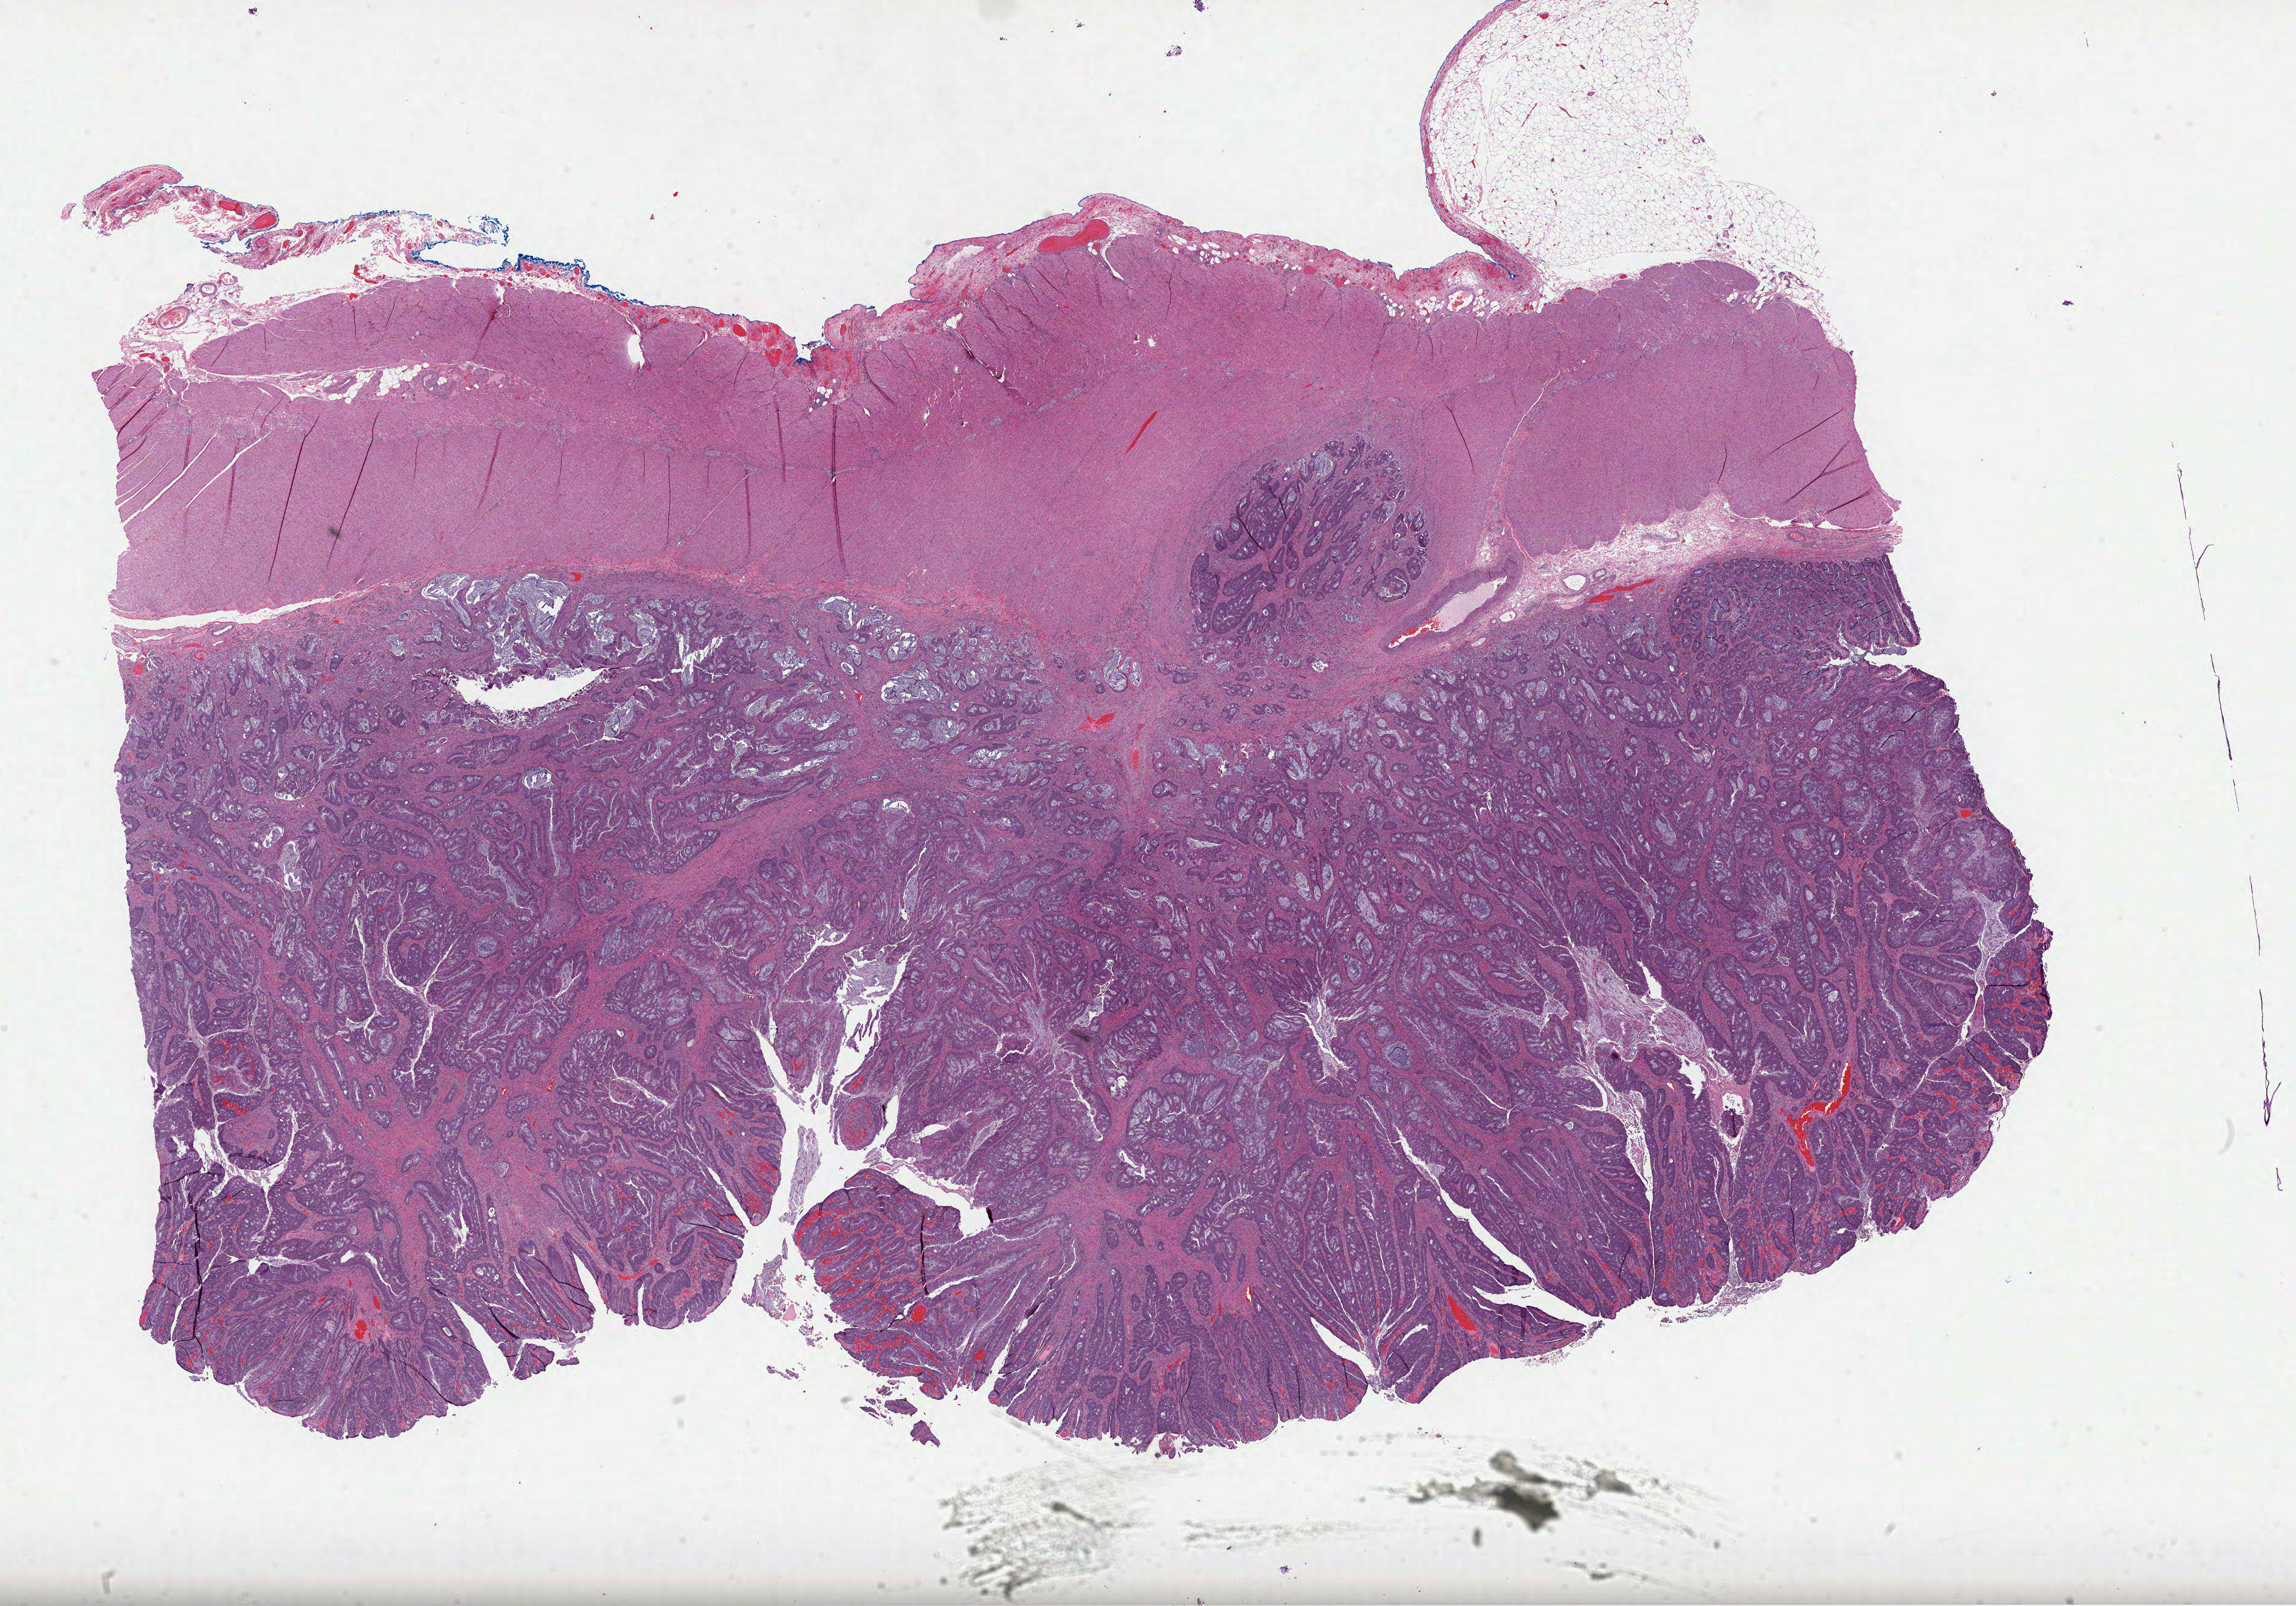
H&E whole-slide image, whole scanned area (about 30.5 x 21.3 mm, from a 40x scan) shown as a low-resolution overview; formalin-fixed paraffin-embedded (FFPE) diagnostic section; sample: primary tumour, rectum. Patient: female, age at initial diagnosis 70 years.
Lymph nodes positive (case pathology): 7 of 24 examined. AJCC pathologic stage: IVA. TNM: T3 N2a M1a. Diagnosis: Adenocarcinoma, NOS.